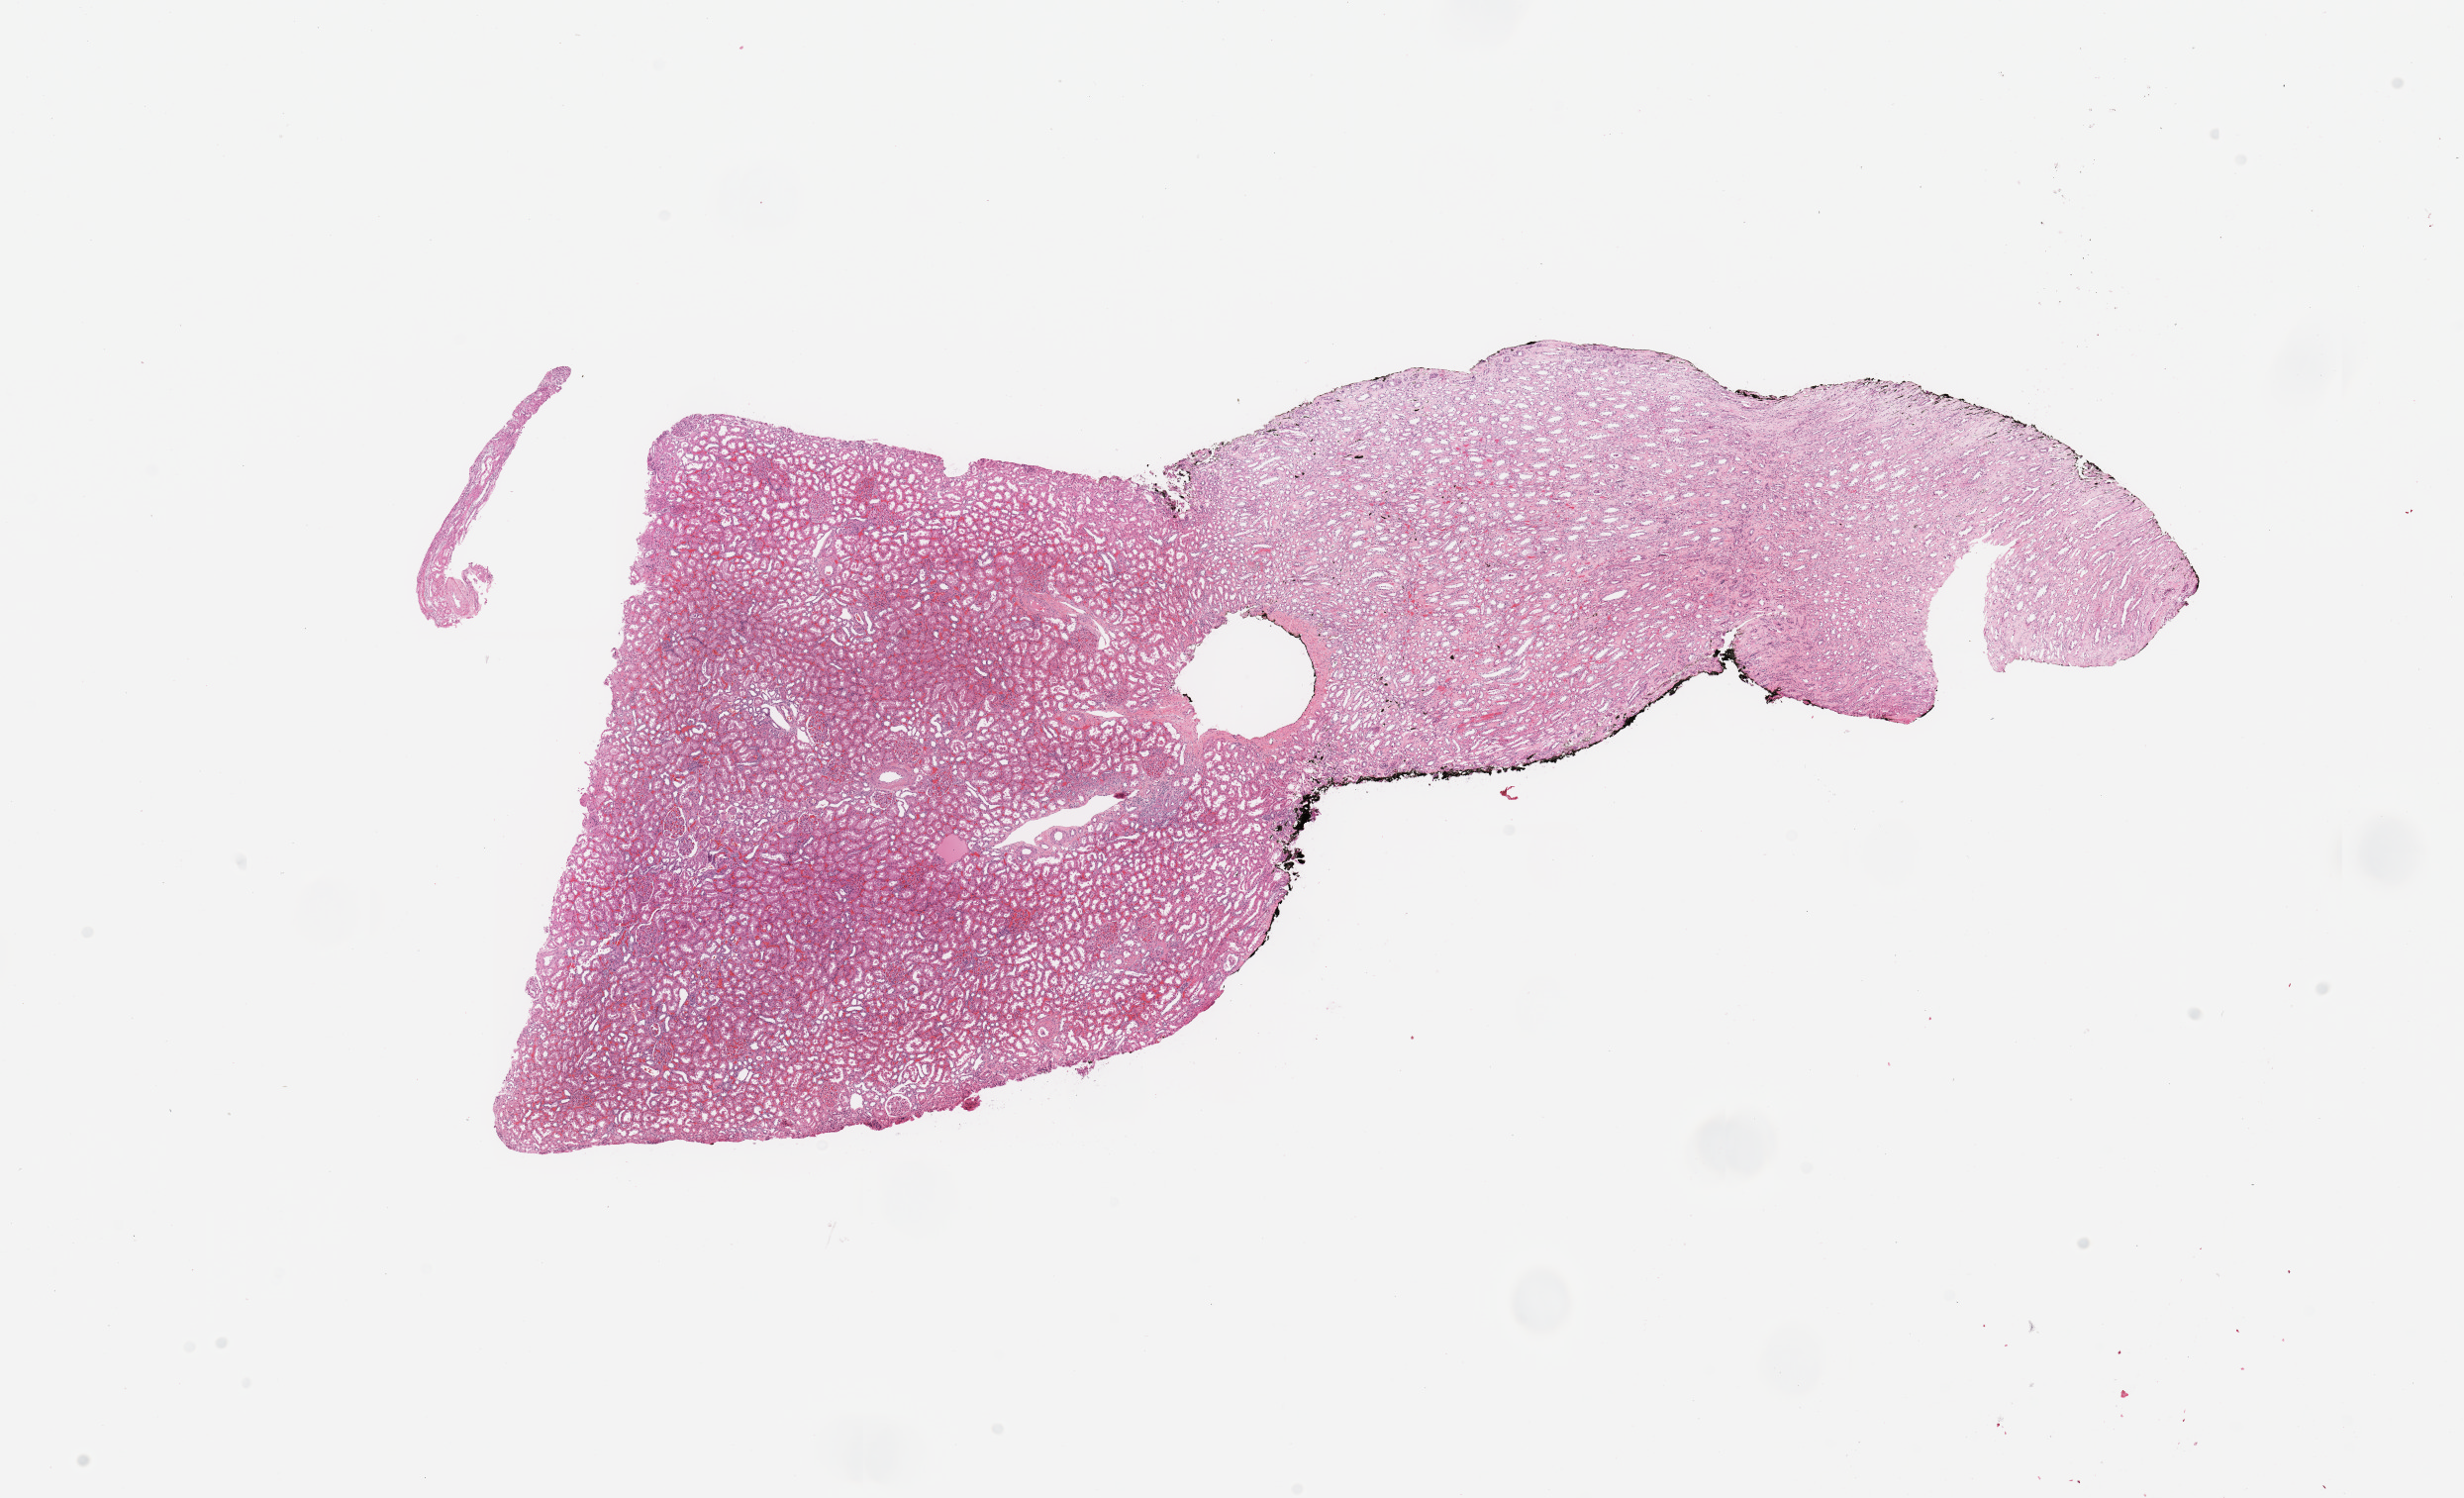
Digitized H&E-stained tissue section (whole slide), shown as a low-resolution overview of the whole scanned area (about 19.7 x 12.0 mm), normal (non-tumour) tissue sample, sampled site: kidney. Male, 47 y/o.
This section: normal (non-tumour) tissue from the same patient. Patient diagnosis: Renal cell carcinoma, NOS.